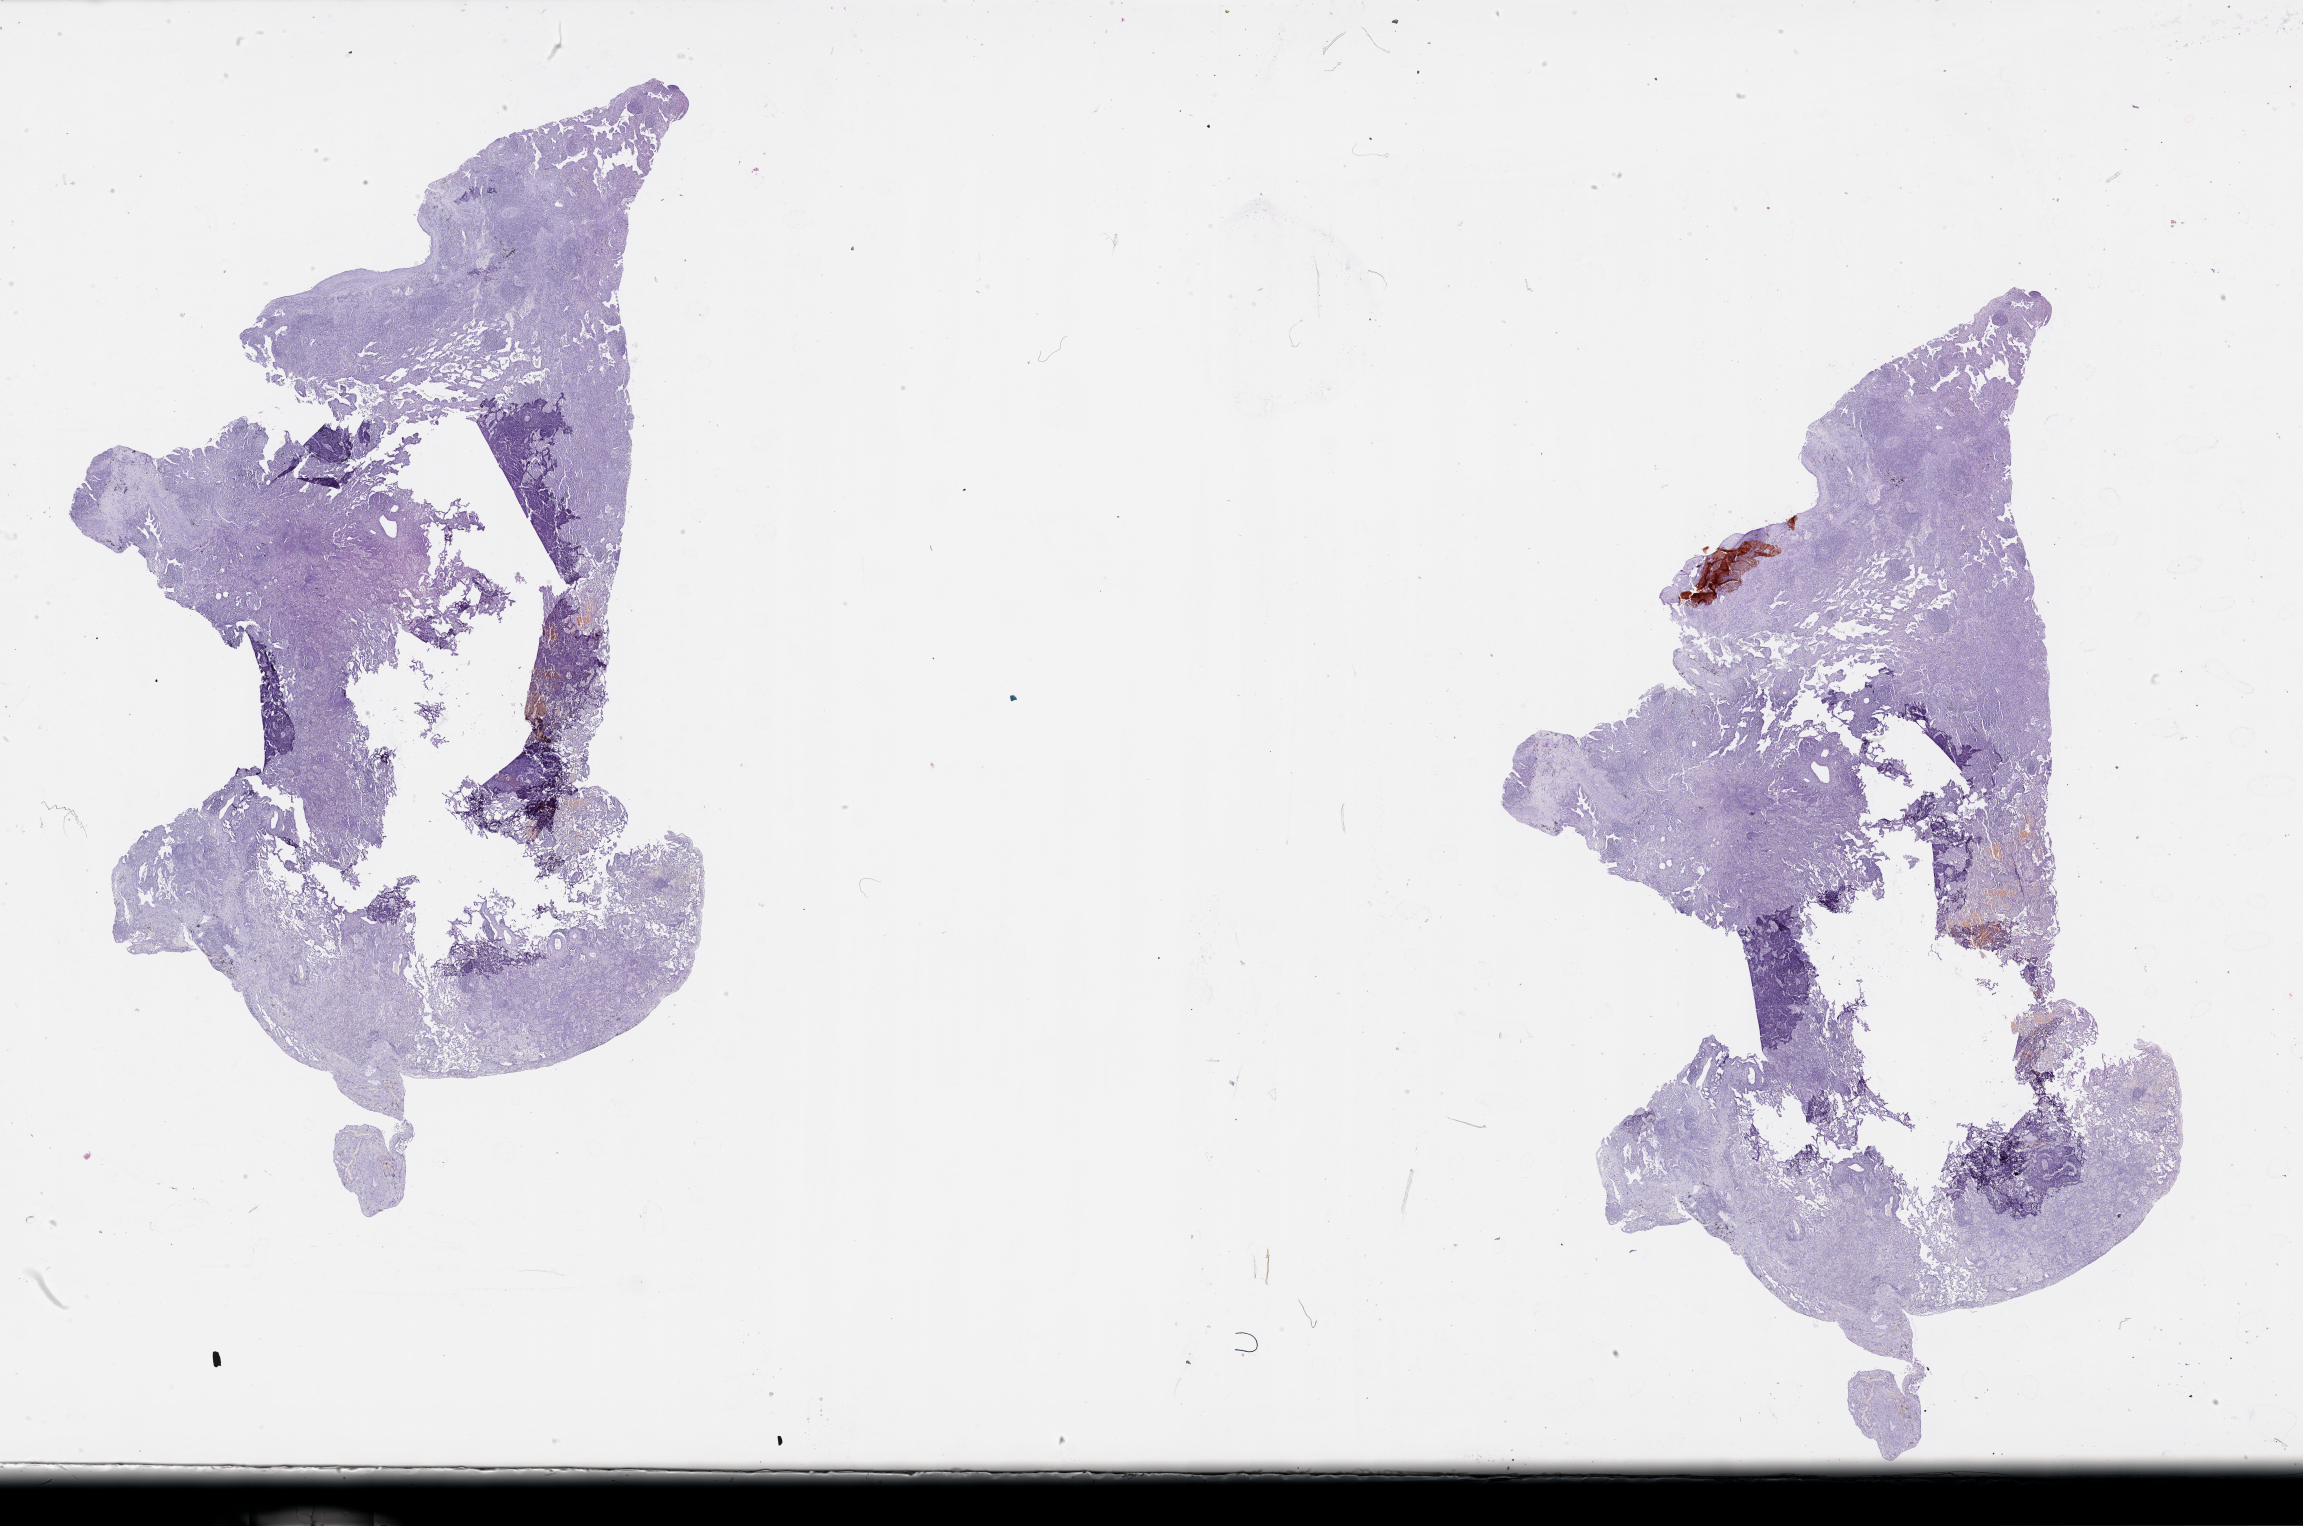
Digitized Hematoxylin and eosin (H&E) stained tissue section (whole slide) — whole scanned area (about 37.1 x 24.6 mm) shown as a low-resolution overview, tumour tissue sample, lung. Male, 70 y/o.
Patient diagnosis (cohort enrolment): squamous cell carcinoma (lung).